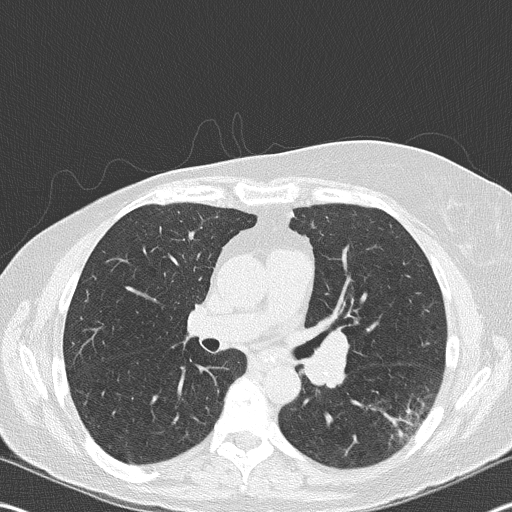
Axial slice from a low-dose chest CT screening exam; second annual screen; lung window (W 1500 / L -600 HU); 120 kVp. Female, age 60 years at enrolment. Current smoker at enrolment.
• Expert-annotated lung lesion, bounding box [x1, y1, x2, y2] px = [375, 380, 447, 452].
• Reader record for this screening exam (exam-level; its link to the box is not recorded): non-calcified nodule or mass ≥4 mm, left lower lobe, 18 × 16 mm, spiculated (stellate) margins, soft tissue attenuation, pre-existing on the prior screen: no.
• Official screen result: positive, other.
• Later outcome: lung cancer diagnosed 35 days after this screen — carcinoma, NOS, left hilum, stage IV (AJCC 6th edition), 45 mm at pathology.